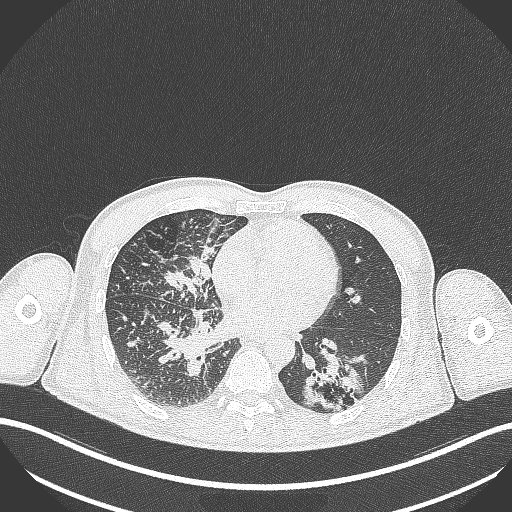
Chest CT, one axial slice; slice 131 of 348 in the series (ordered by position); reconstruction kernel B70f; lung window (W 1500 / L -600 HU); 1 mm slice thickness; 512 × 512 image matrix, field of view 400 × 400 mm. Patient: male, 49 years. Case-level facts recorded for this patient, not image findings: clinical TNM (as recorded): T2b N1 M0.
Structures marked on this image (rectangle marked by the reading radiologist):
- lung tumour (recorded histology: adenocarcinoma): box from (x=297, y=350) to (x=365, y=413) px